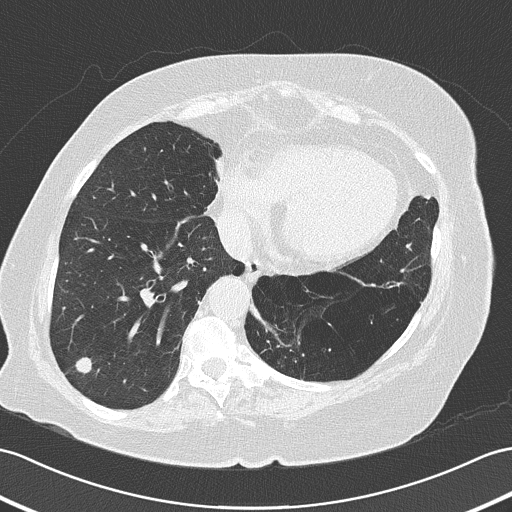
Chest CT (low-dose screening protocol), one axial image, baseline annual screen, lung window (W 1500 / L -600 HU), 2 mm slice thickness, lung (sharp) reconstruction kernel (B50f), 512 × 512 image matrix. Female participant, aged 73 years at enrolment. Former smoker at enrolment.
• Expert reader's lesion annotation, bounding box <53,336,101,384> (left, top, right, bottom; pixels).
• The screening reader recorded 4 non-calcified nodules or masses ≥4 mm on this exam (right lower lobe, right upper lobe, left upper lobe, left lower lobe); which of them this box marks is not recorded.
• Lung cancer was diagnosed 50 days after this screen: adenocarcinoma, NOS, right lower lobe, poorly differentiated (G3), stage IB (AJCC 6th edition), 17 mm at pathology.